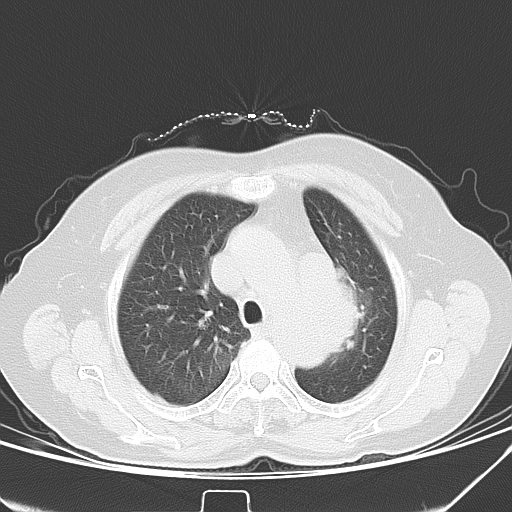
Chest CT, one axial slice. Slice 31 of 40 in the series (ordered by position). 120 kVp. Lung window (W 1500 / L -600 HU). 5 mm slice thickness. 512 × 512 image matrix, field of view 331 × 331 mm. Patient: female, 59 years. From the clinical record (not read from this slice): clinical TNM (as recorded): T3 N1 M0; histopathological grade: G3.
Annotated regions visible in this slice (bounding box drawn by a radiologist):
- lung tumour (recorded histology: small cell carcinoma): bounding box [x1, y1, x2, y2] px = [339, 262, 370, 367]